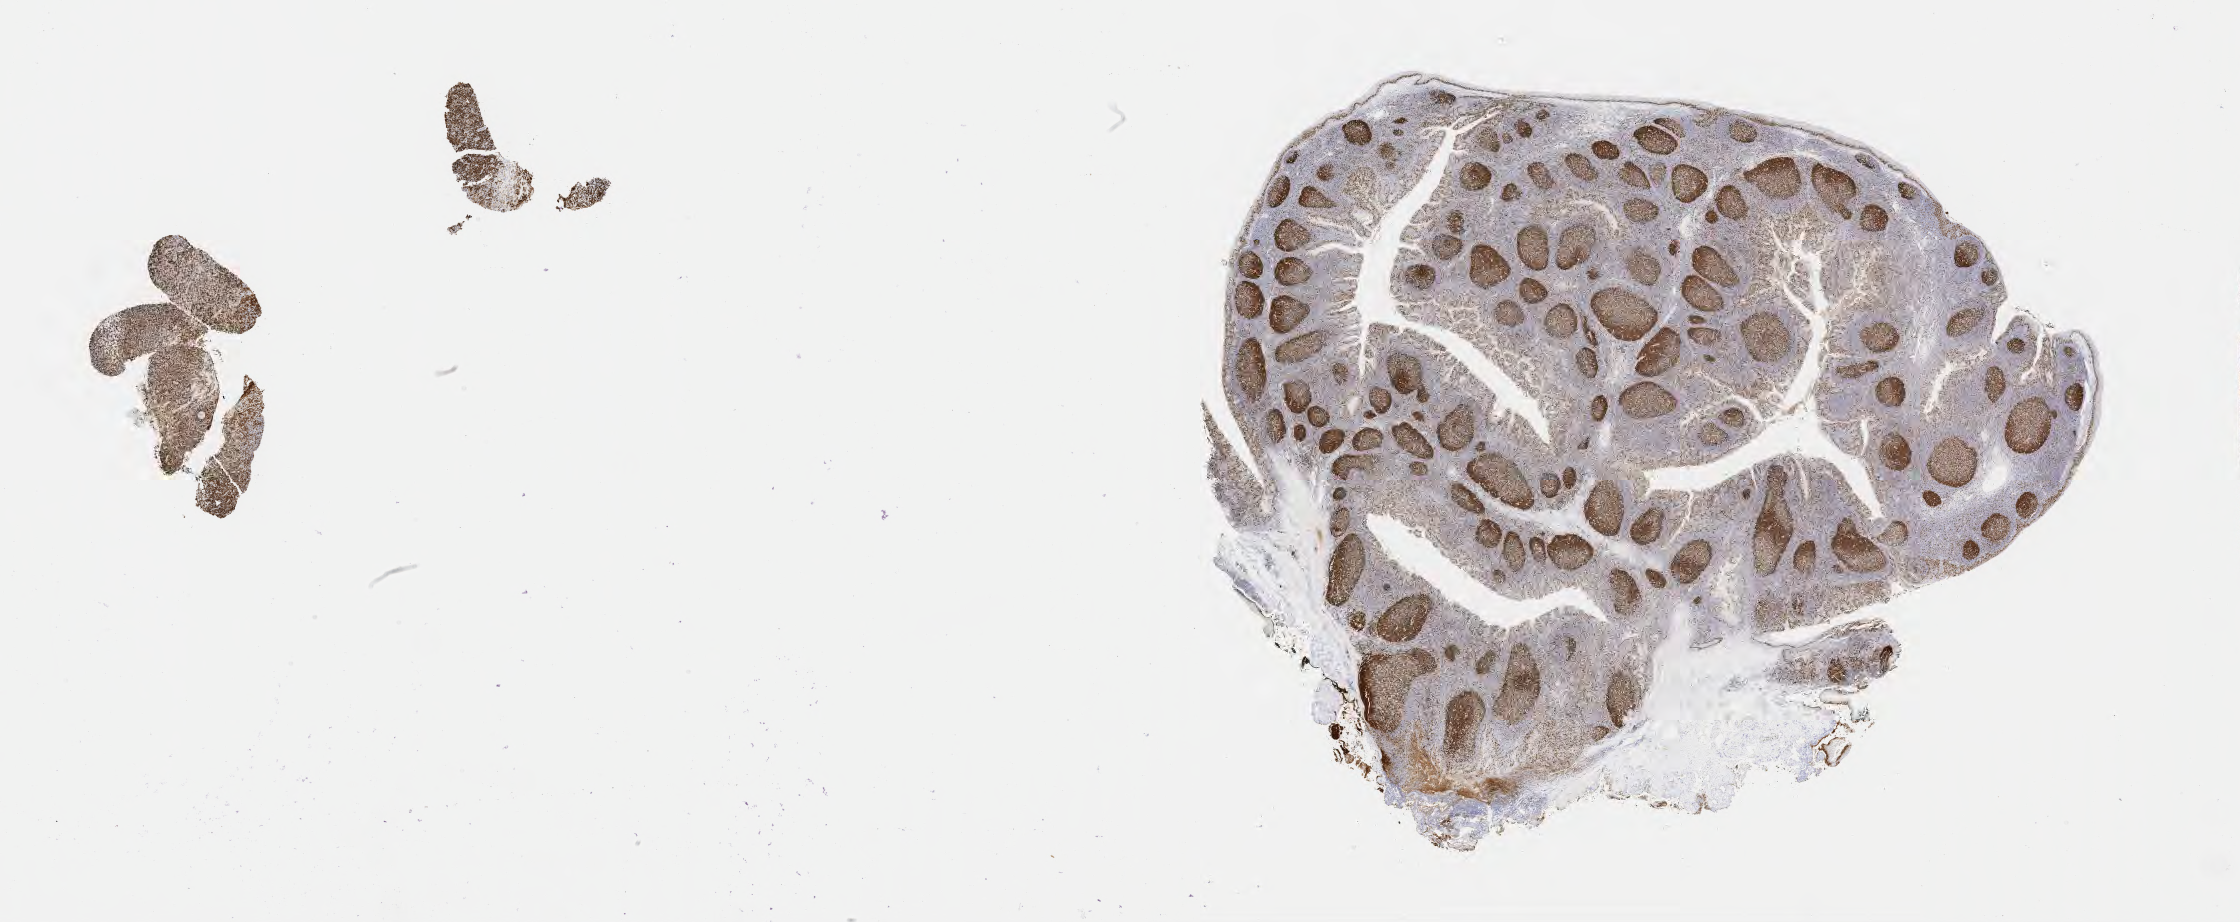
Immunohistochemistry (IHC) whole-slide image stained for Ki-67 — a low-resolution overview of the entire scanned area, about 36.2 x 14.9 mm, specimen: tumor tissue, anatomic site: lymph node. Patient: male, age 54 years.
Diagnosis: Diffuse large B-cell lymphoma, NOS.